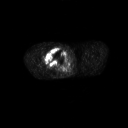
FDG PET of an extremity soft-tissue mass (from a PET/CT study), one axial slice. Slice 255 of 311 in the series (ordered by position). 128 × 128 image matrix. Patient: male, 50 years. From the clinical record (not read from this slice): histological type: undifferentiated - pleiomorphic; grade: high; site of the primary tumour: right thigh.
Annotated regions visible in this slice (expert contour drawn on MRI and transferred to this co-registered scan by the dataset authors):
- gross tumour volume including surrounding oedema: bounding box <42,48,66,67> (left, top, right, bottom; pixels)
- gross tumour volume (mass): <45,48,66,67>